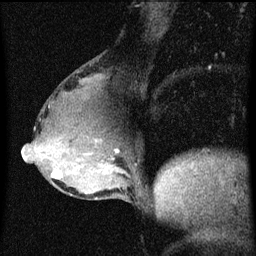
Breast MRI (dynamic contrast-enhanced), one sagittal slice; position 29 of 60 along the scan axis; dynamic contrast-enhanced series, image 2 of 3 at this slice position (ordered by acquisition); 1.5 T; TE 4.2 ms, TR 8 ms; 2 mm slice thickness; 256 × 256 image matrix, field of view 180 × 180 mm. Female patient, age 49 years.
Outlined on this slice (semi-automatic segmentation, software-assisted and operator-edited):
- analysis volume of interest (the breast-tissue region the enhancement analysis was run in; not a lesion): bounding box <51,158,96,185> (left, top, right, bottom; pixels)
- tumour enhancement mask (voxels above the 70 % enhancement threshold inside the analysis volume of interest): <52,170,63,179>